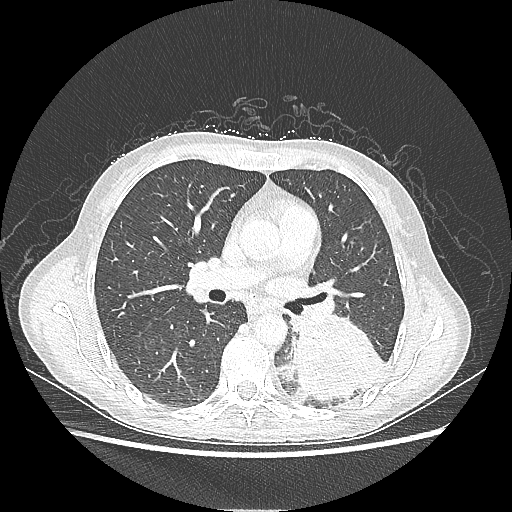
Chest CT, one axial slice; slice 123 of 220 in the series (ordered by position); reconstruction kernel LUNG; 80 kVp; lung window (W 1500 / L -600 HU); 1.25 mm slice thickness; 512 × 512 image matrix, field of view 360 × 360 mm. Patient: female, 53 years. Case-level facts recorded for this patient, not image findings: clinical TNM (as recorded): T3 N0 M0.
Annotated regions visible in this slice (rectangle marked by the reading radiologist):
- lung tumour (recorded histology: adenocarcinoma): bounding box [x1, y1, x2, y2] px = [287, 314, 386, 403]